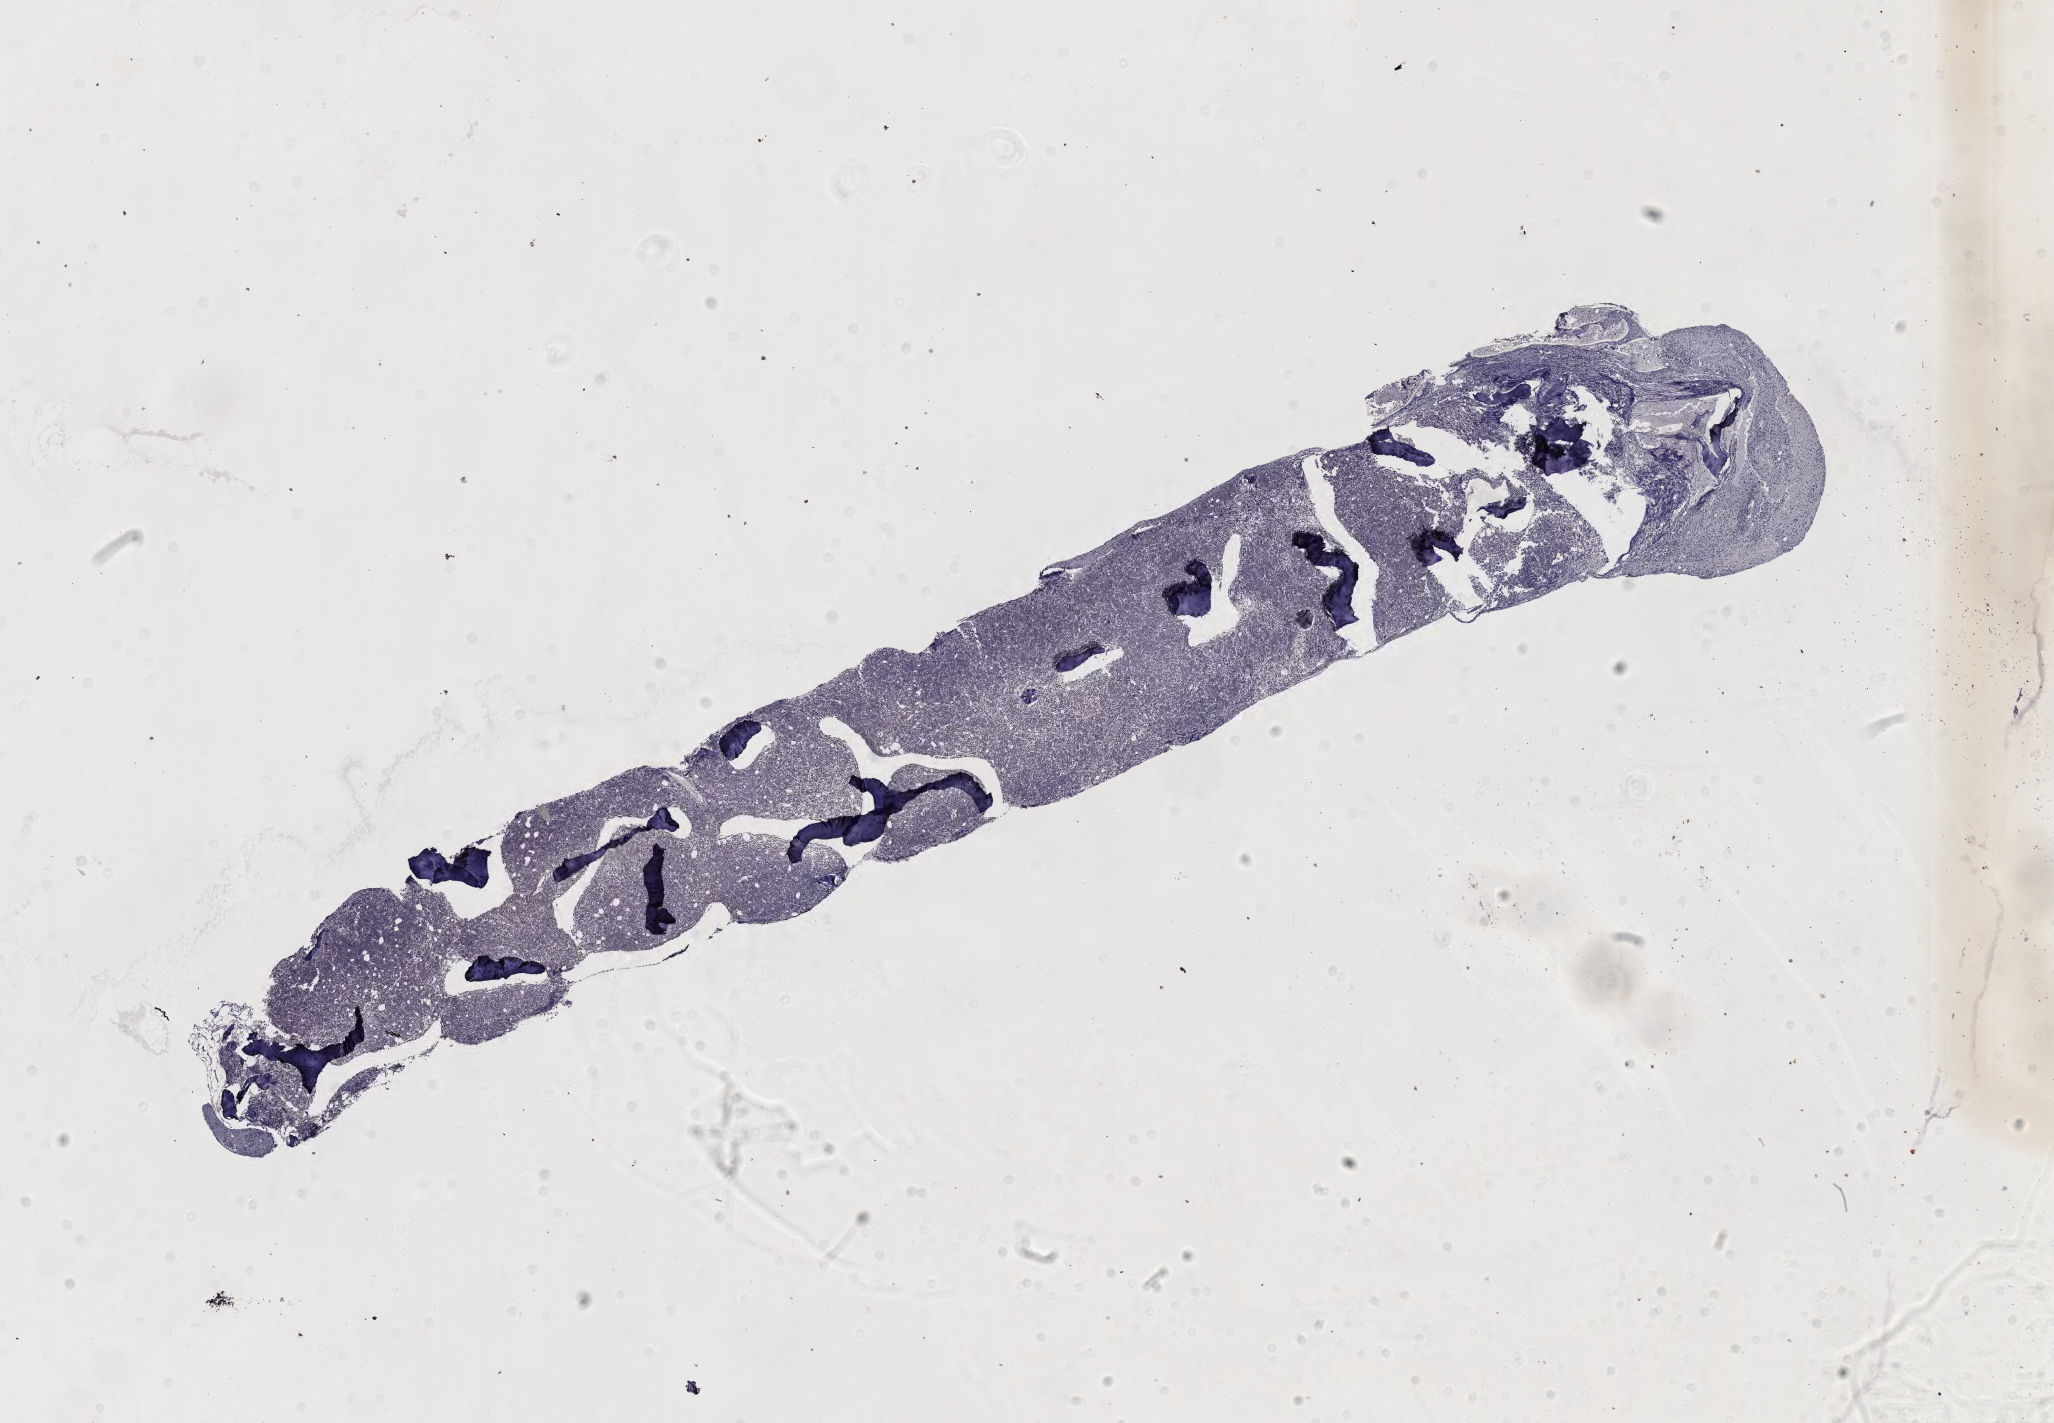
Immunohistochemistry (IHC) whole-slide image stained for BCL6 — low-resolution overview of the scanned area, about 16.6 x 11.5 mm, specimen: tumor tissue. Patient female; aged 64.
Histologic diagnosis: Burkitt lymphoma, NOS.